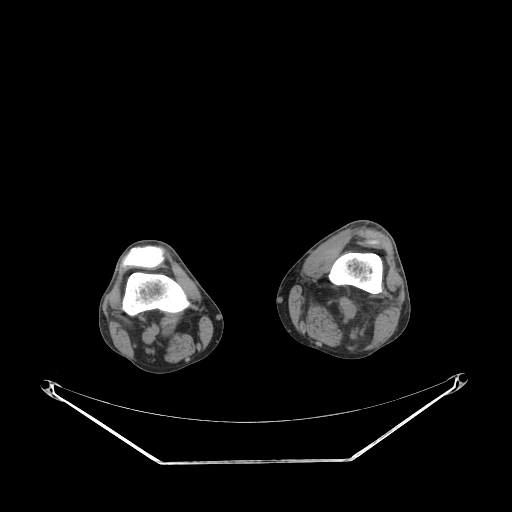
CT of an extremity soft-tissue mass (from a PET/CT study), one axial slice; slice 195 of 267 in the series (ordered by position); 140 kVp; soft-tissue window (W 400 / L 40 HU); 512 × 512 image matrix. Male patient. From the clinical record (not read from this slice): histological type: undifferentiated pleomorphic liposarcoma; grade: high; site of the primary tumour: left thigh.
Structures marked on this image (expert contour drawn on MRI and transferred to this co-registered scan by the dataset authors):
- gross tumour volume including surrounding oedema: box from (x=301, y=295) to (x=316, y=316) px